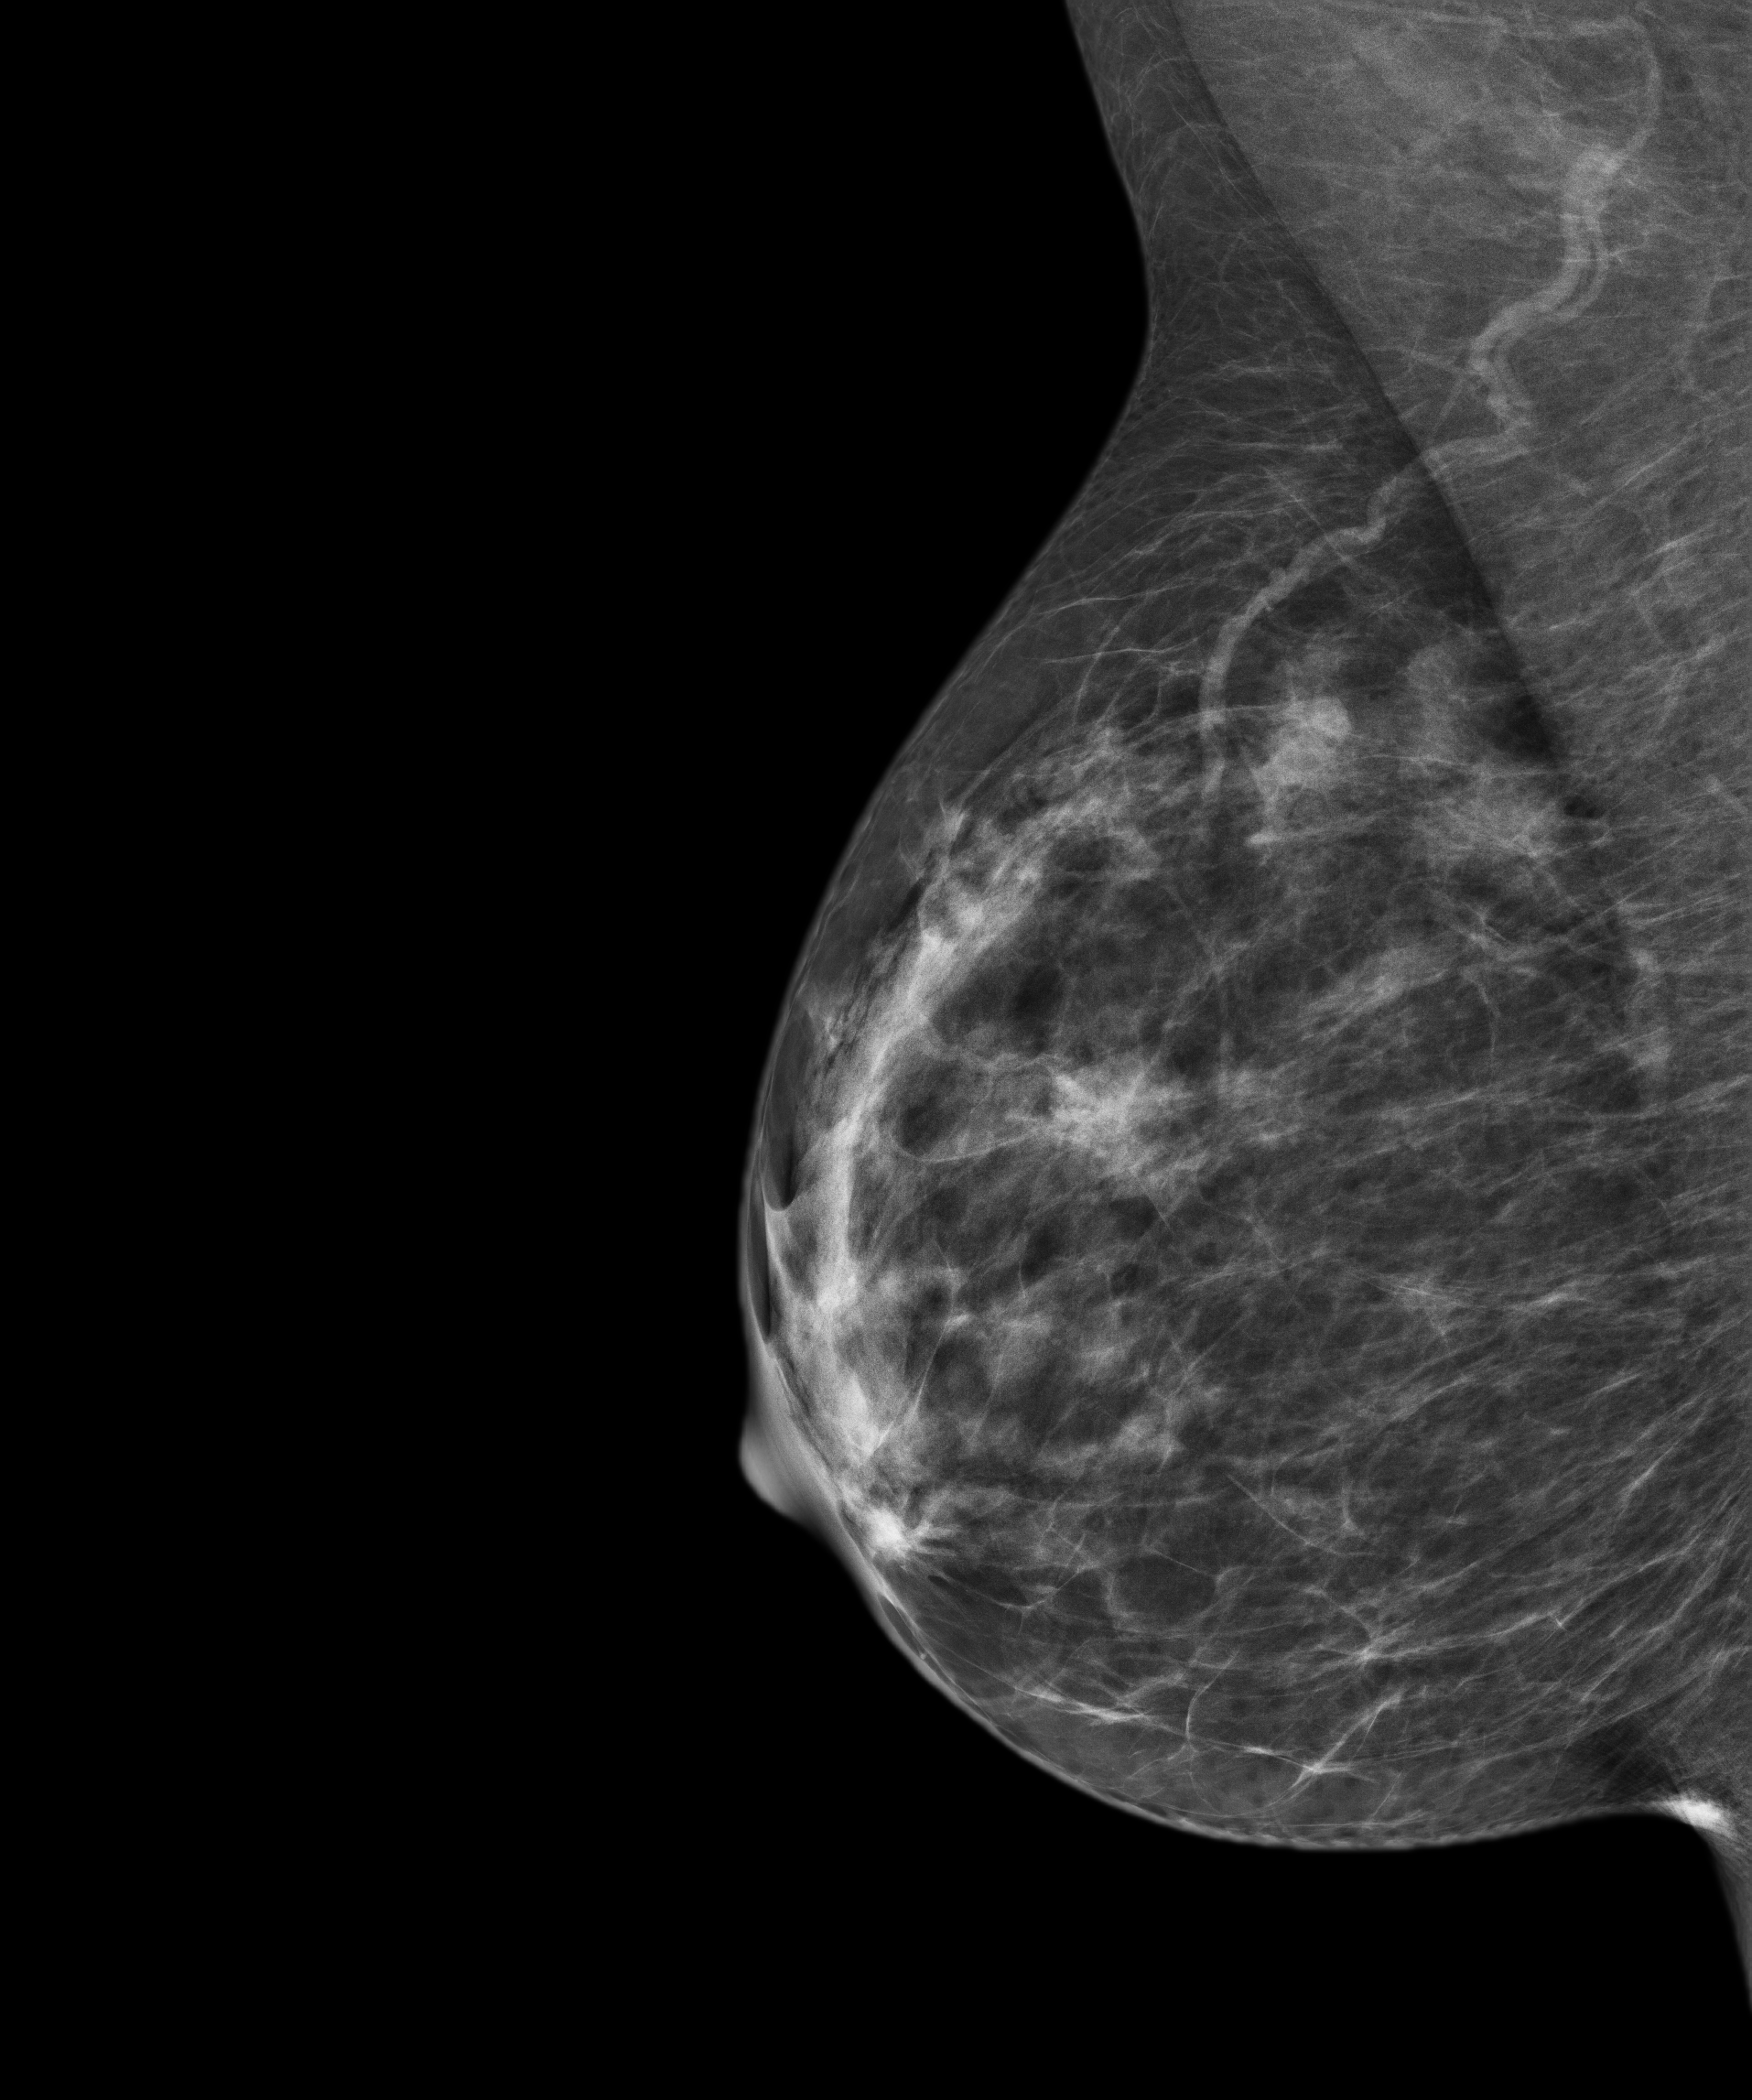
Digital mammogram (FFDM), right breast, MLO view, annual screening mammography examination, compressed breast thickness 32 mm, system: Senographe Pristina. Patient: female, 43 years.
Breast density at the screening exam (both breasts): heterogeneously dense (BI-RADS density category c). Final BI-RADS assessment for this screening round (tomosynthesis exam, both breasts): category 1. Recall: no recall after this screen.